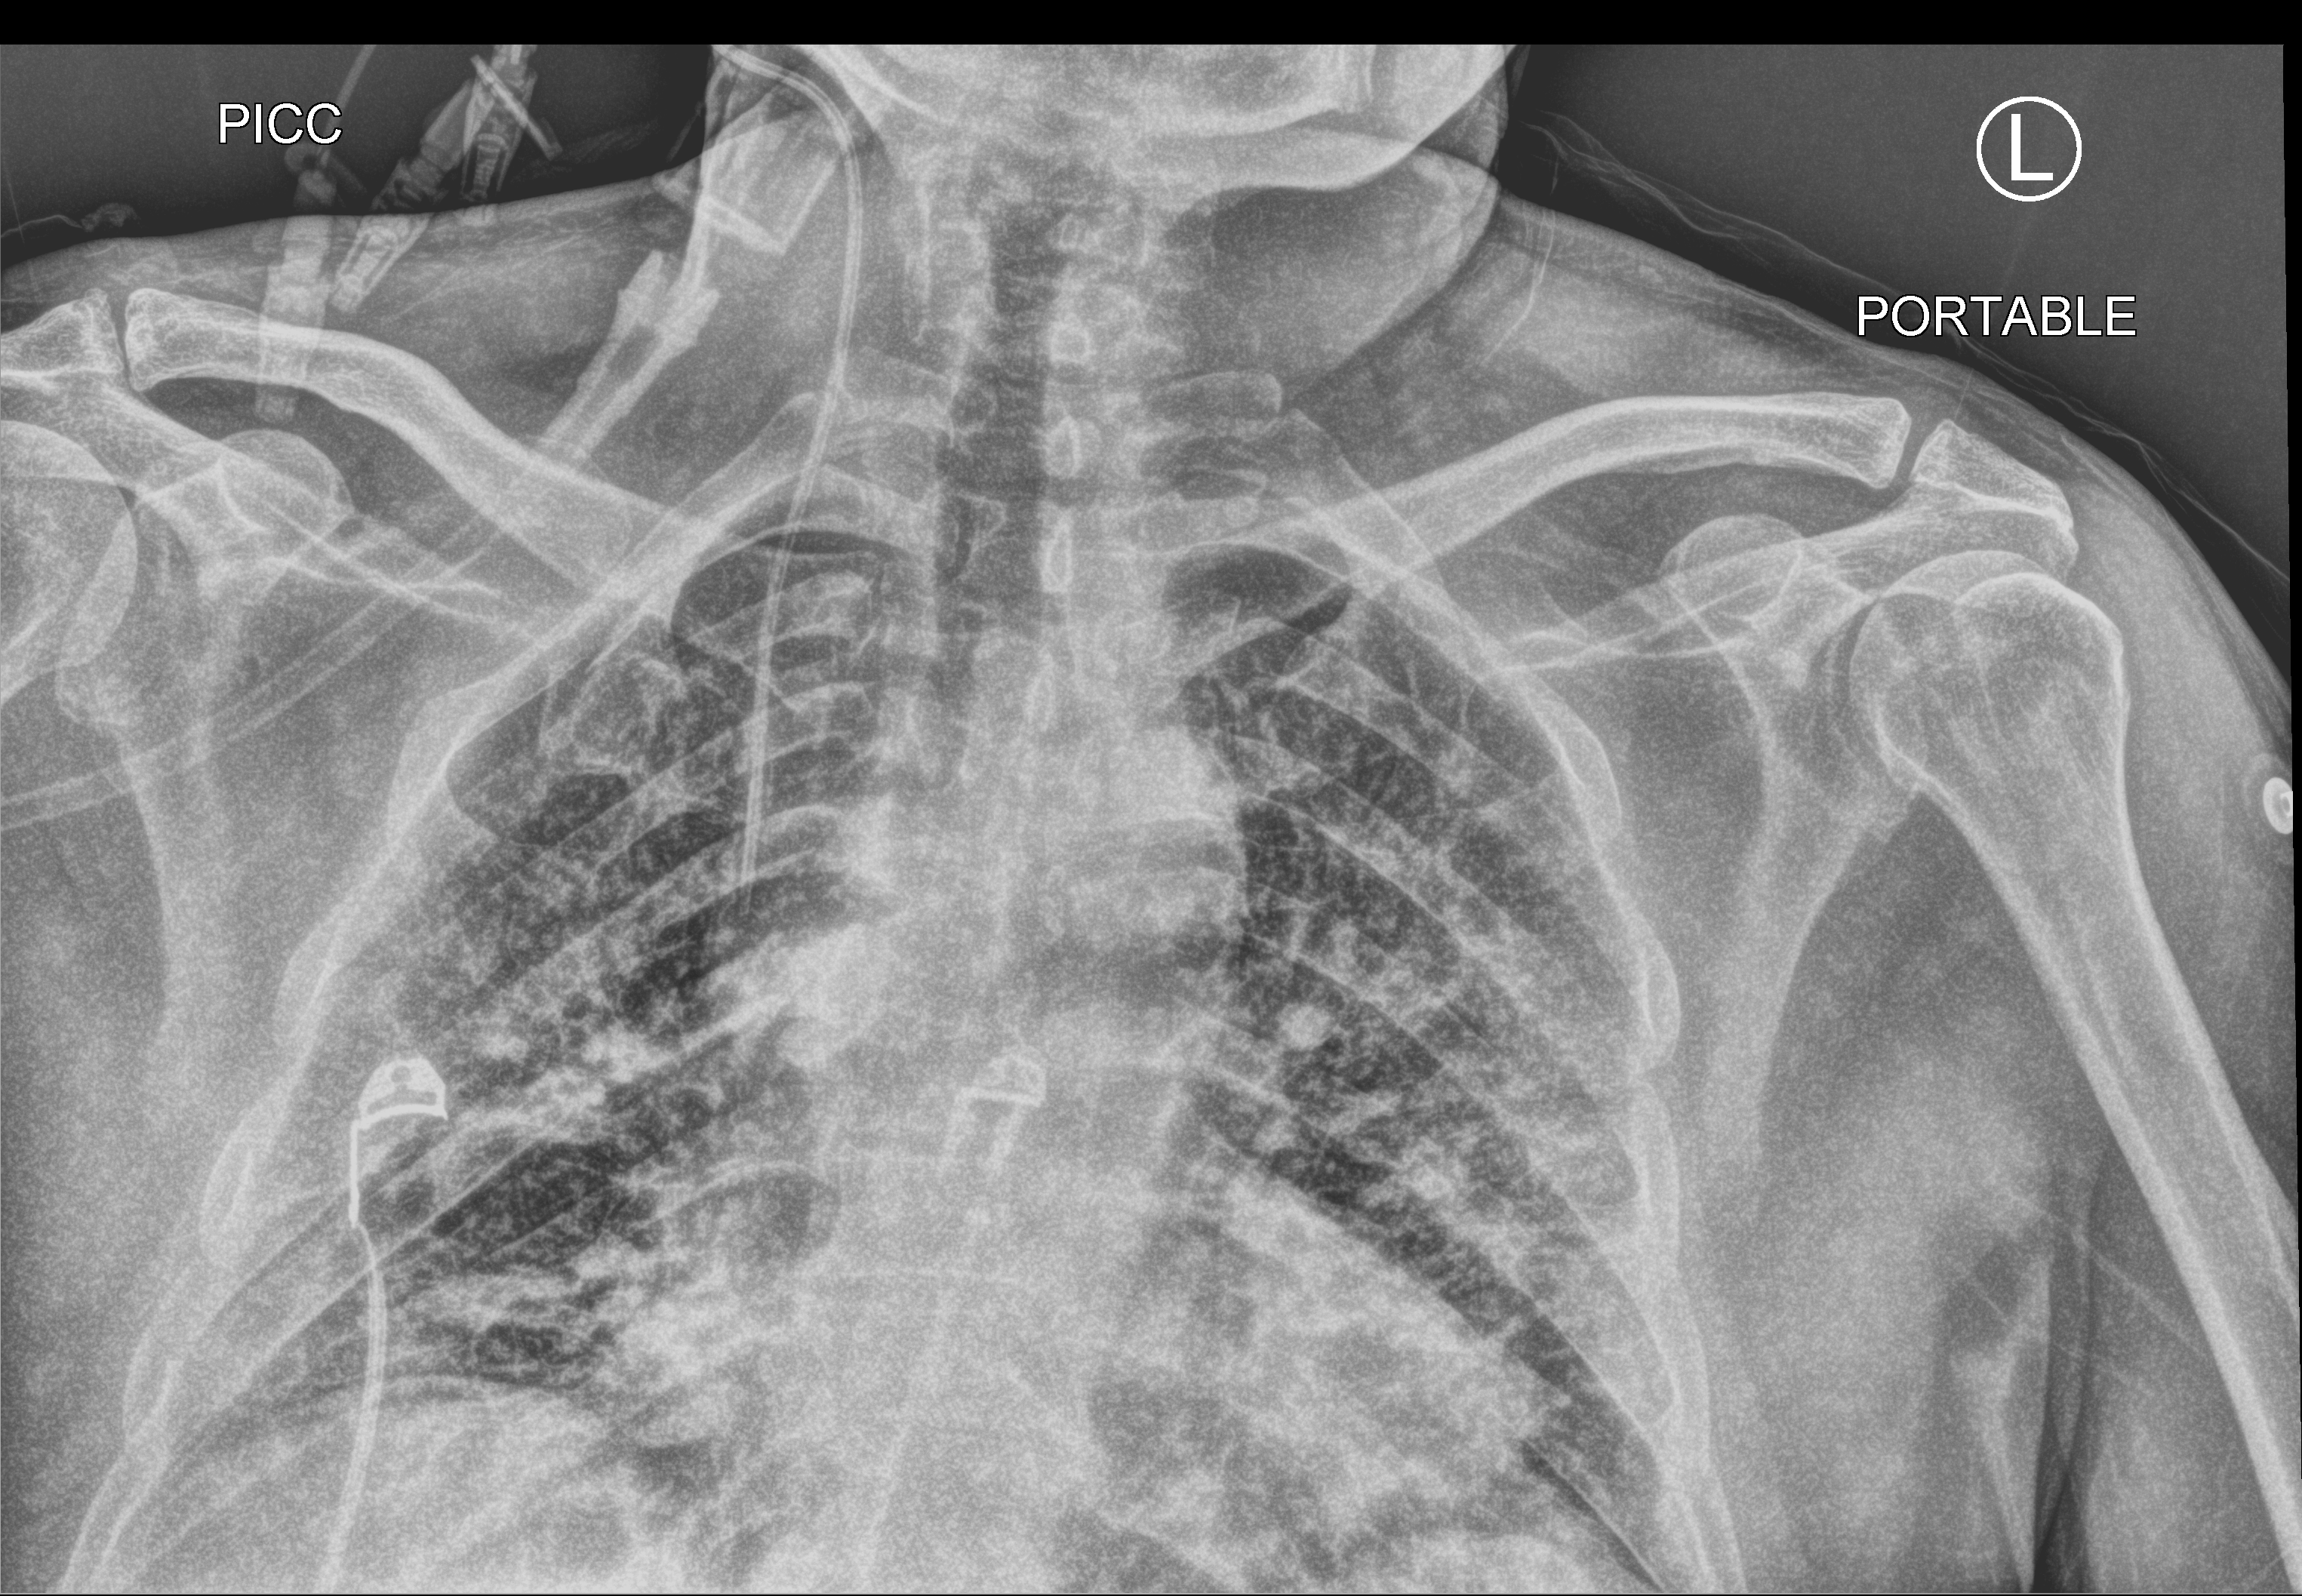
Chest X-ray (portable), anteroposterior (AP) projection. Male patient hospitalised with COVID-19, age 60–74 years.
From the hospital-stay record, not from the radiograph (when in the stay this image was taken is not recorded):
- length of hospital stay: 32 days
- admitted to intensive care during this hospital stay: yes